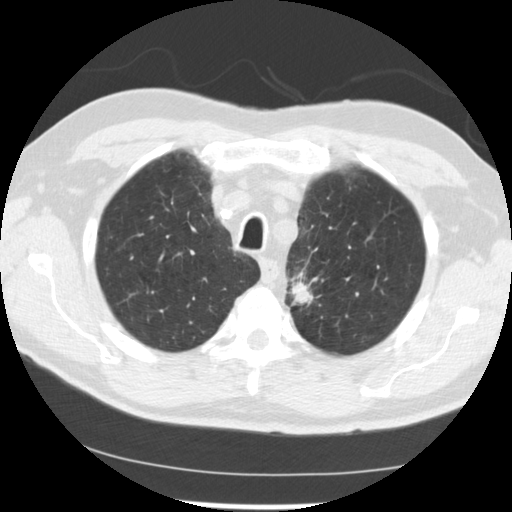
Axial slice from a low-dose chest CT screening exam, baseline screening round, lung window (W 1500 / L -600 HU), standard (soft-tissue) reconstruction kernel (STANDARD), slice 200 of 249 in the series, 512 × 512 image matrix. Male, age 71 years at enrolment. Current smoker at enrolment.
Expert-annotated lung lesion, bounding box <274,262,334,317> (left, top, right, bottom; pixels). The screening reader recorded 2 non-calcified nodules or masses ≥4 mm on this exam (left upper lobe, left upper lobe); which of them this box marks is not recorded. Official screen result: positive, change unspecified: nodule(s) >= 4 mm or enlarging nodule(s), mass(es), or other non-specific abnormalities suspicious for lung cancer. Lung cancer was diagnosed 37 days after this screen: adenocarcinoma, NOS, left upper lobe, poorly differentiated (G3), stage IIIB (AJCC 6th edition), 25 mm at pathology.